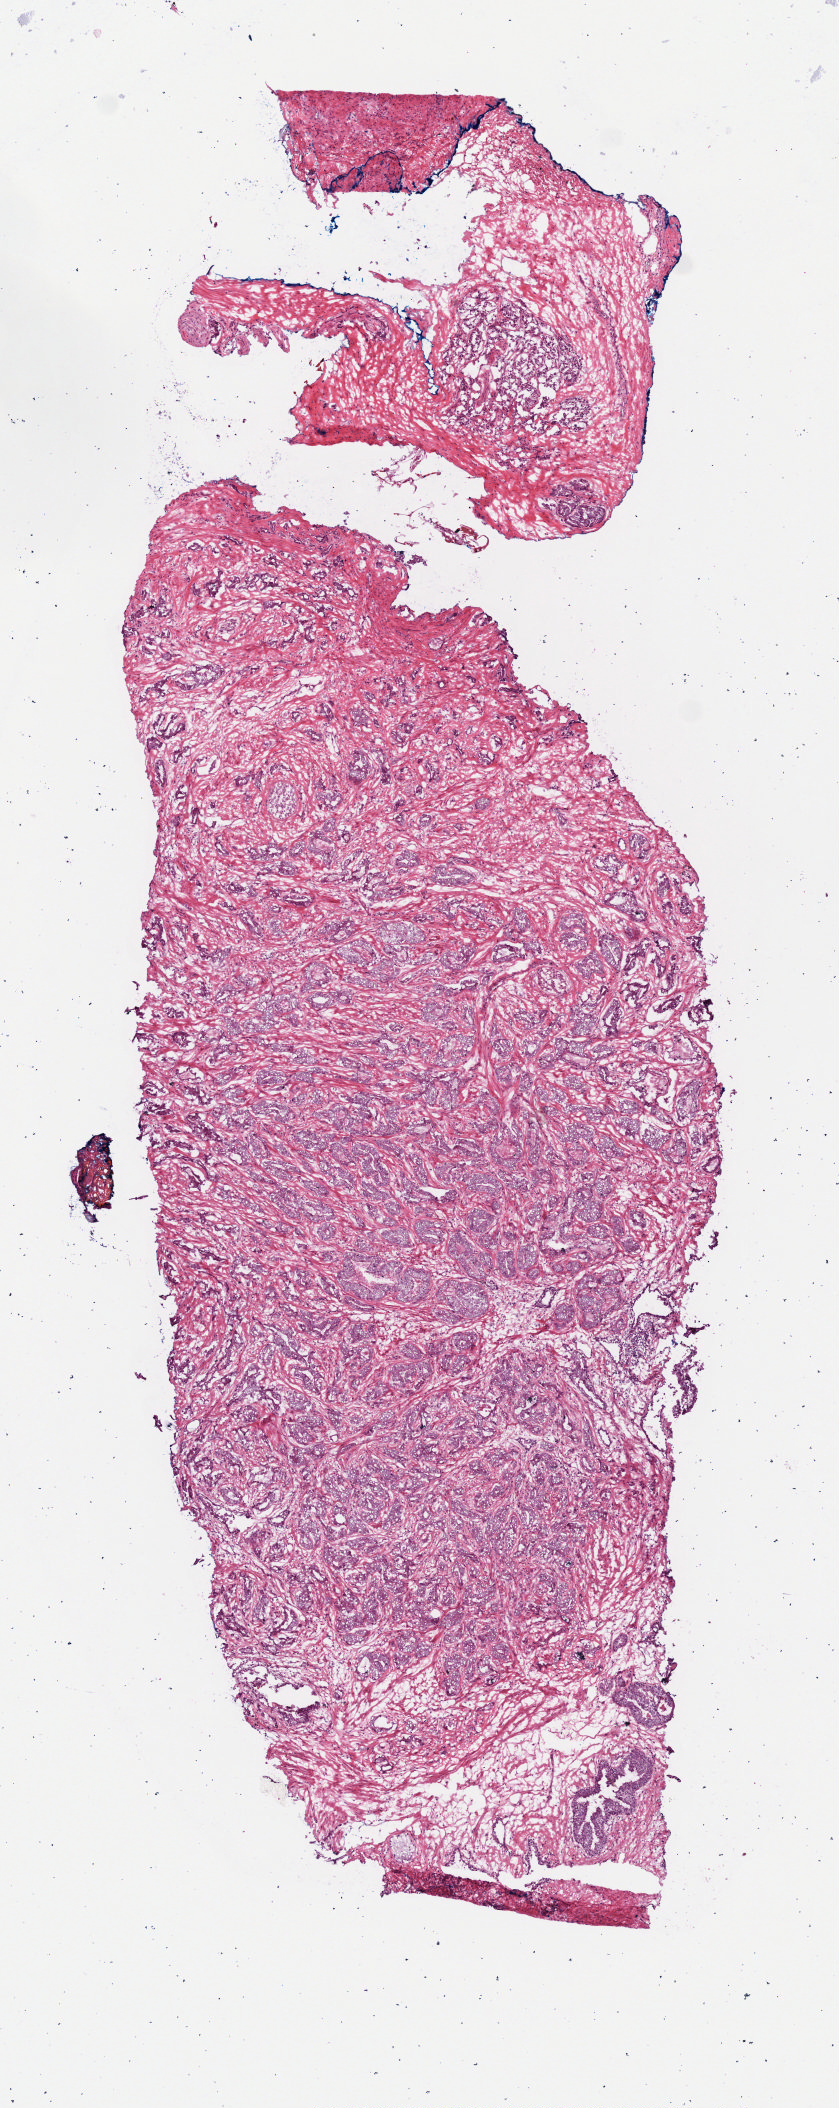
Whole-slide histology image, H&E, whole scanned area (about 3.4 x 8.5 mm, from a 40x scan) shown as a low-resolution overview, frozen section from the top of the tissue portion, sample: primary tumour, prostate. Patient: male, age at initial diagnosis 67 years. Gleason score: 7 (4+3). Slide review estimates, as recorded: tumour cells 80%, tumour nuclei 85%, normal cells 2%, stromal cells 18%, necrosis 0%. Inflammatory infiltration, as recorded: lymphocyte infiltration 0%, monocyte infiltration 0%, neutrophil infiltration 0%.
• histologic diagnosis: Adenocarcinoma, NOS (prostate gland)